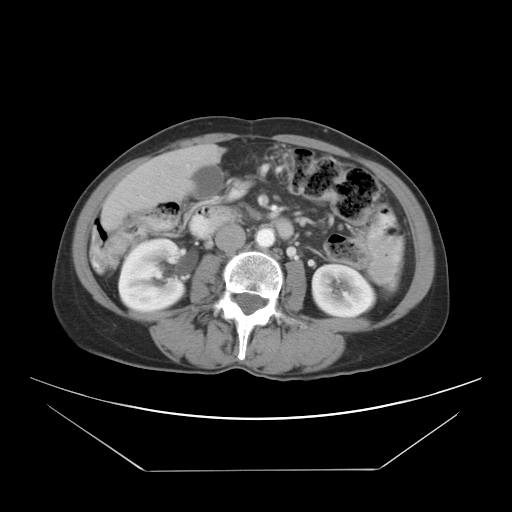
Contrast-enhanced abdominal CT, one axial slice. Reconstruction kernel STANDARD. 120 kVp. Soft-tissue window (W 400 / L 40 HU). 7.5 mm slice thickness. 512 × 512 image matrix, field of view 412 × 412 mm. Female patient, age 54 years. From the clinical record (not read from this slice): diagnosis: colorectal cancer liver metastases, imaged before liver resection; multiple liver metastases: yes; largest metastasis: 2.5 cm; disease in both lobes: yes.
Annotated regions visible in this slice (outlined manually by an expert reader):
- liver: bounding box (x1, y1, x2, y2) in pixels: (104, 147, 217, 226)
- planned liver remnant (the part of the liver to remain after resection): (123, 147, 217, 198)